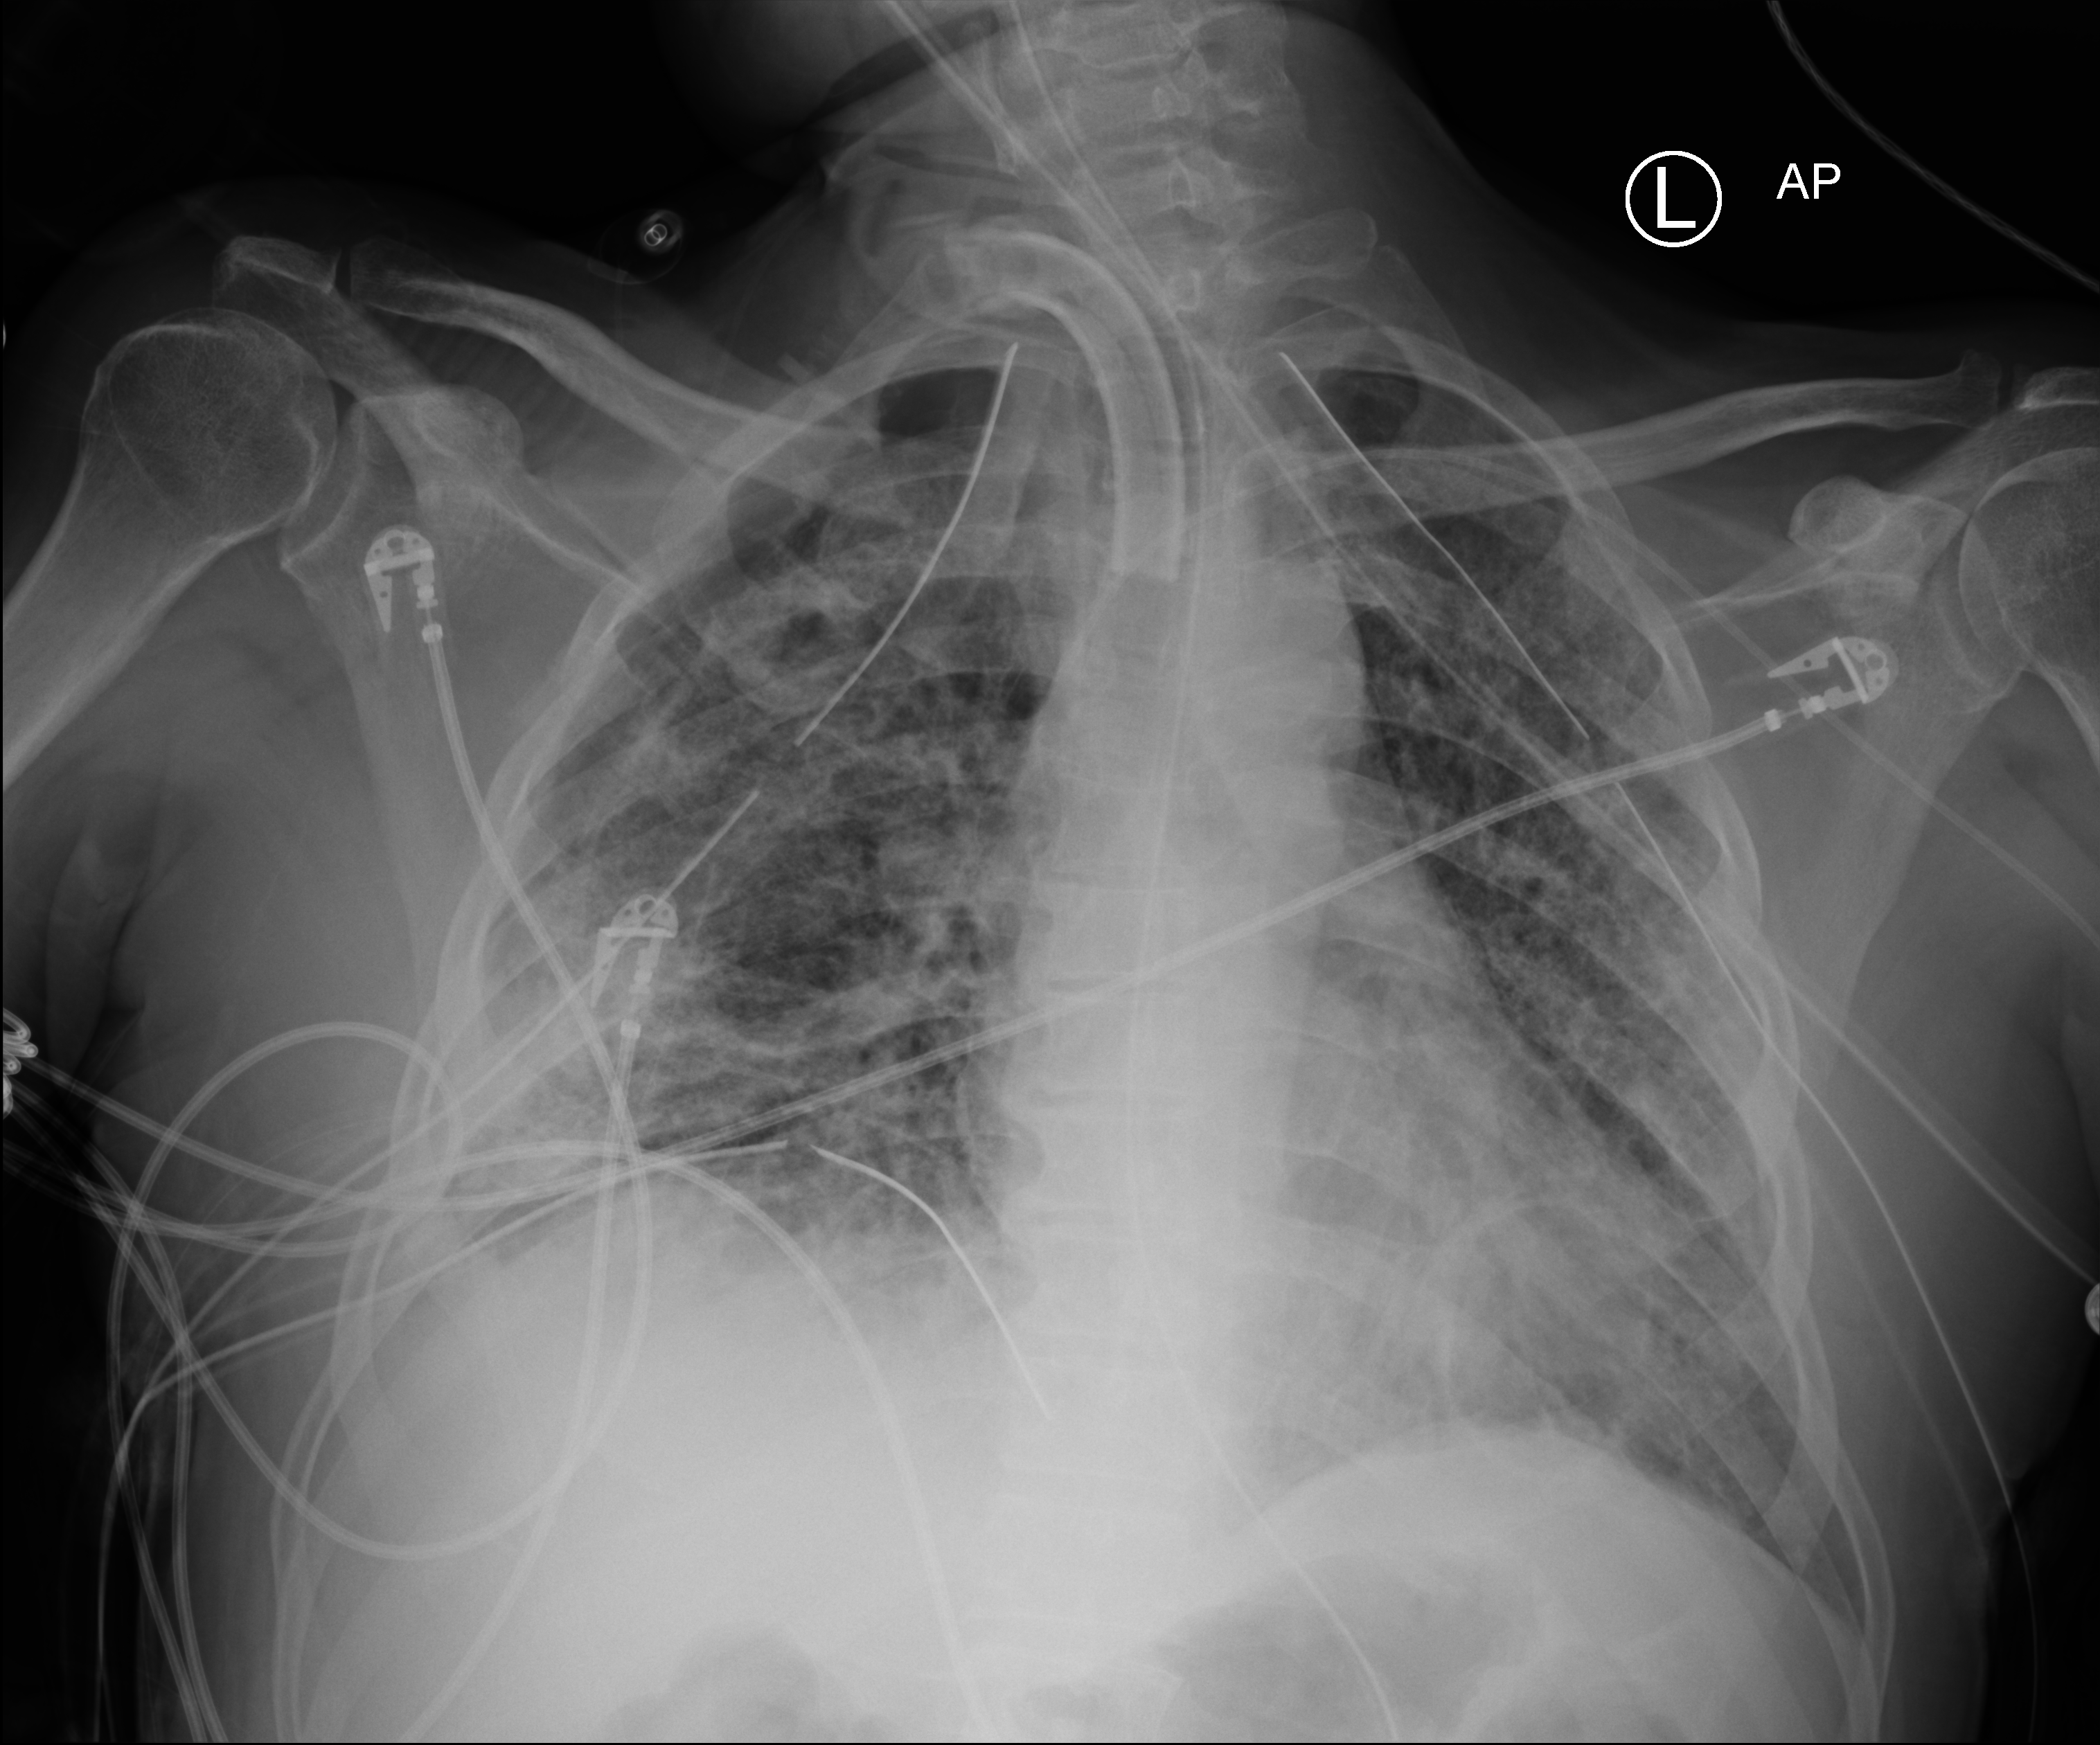
Chest X-ray (portable), anteroposterior (AP) projection. Patient hospitalised with COVID-19; male, aged 18–59 years.
Hospital-stay facts (about this admission, not read from this image; timing relative to this image not recorded): hypertension (admission record): yes.